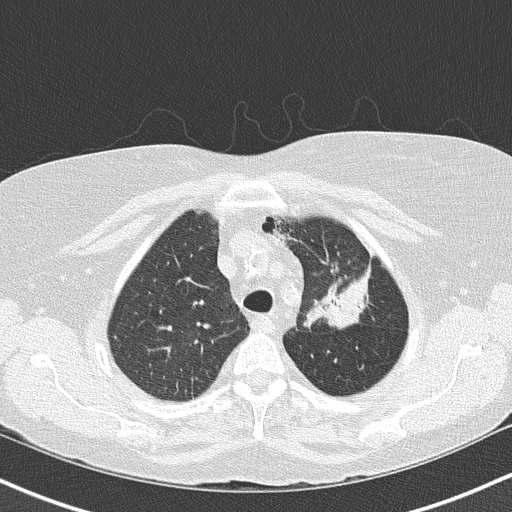
Low-dose screening chest CT, one axial slice. Position 120 of 147 along the scan axis. Reconstruction kernel B50f. 120 kVp. Lung window (W 1500 / L -600 HU). 2 mm slice thickness. 512 × 512 image matrix, field of view 320 × 320 mm.
Structures marked on this image (expert manual segmentation):
- lesion 1 (tumor, upper lobe of left lung): bounding box [x1, y1, x2, y2] px = [306, 274, 367, 328]